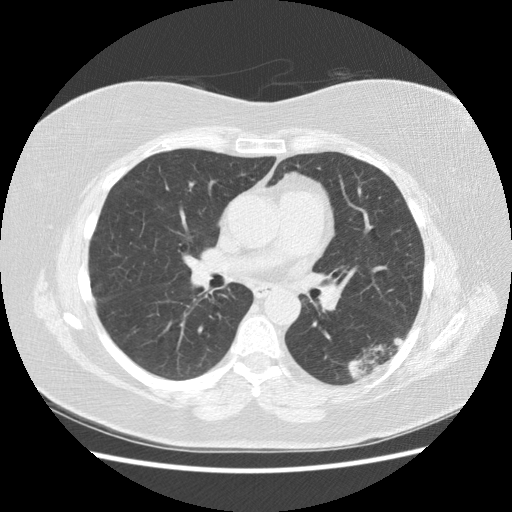
Low-dose screening chest CT, axial slice; third annual screen; lung window (W 1500 / L -600 HU); 2.5 mm slice thickness; 120 kVp; 512 × 512 image matrix. Female, age 57 years at enrolment. Current smoker at enrolment.
Expert-annotated lung lesion, bounding box (x1, y1, x2, y2) in pixels: (332, 325, 411, 387). Reader record for this screening exam (exam-level; its link to the box is not recorded): non-calcified nodule or mass ≥4 mm, left lower lobe, 40 × 20 mm, poorly defined margins, mixed attenuation, pre-existing on the prior screen: yes; interval growth: yes. Official screen result: positive, other. Lung cancer was diagnosed 55 days after this screen: squamous cell carcinoma, NOS, left lower lobe, poorly differentiated (G3), stage IB (AJCC 6th edition), 40 mm at pathology.